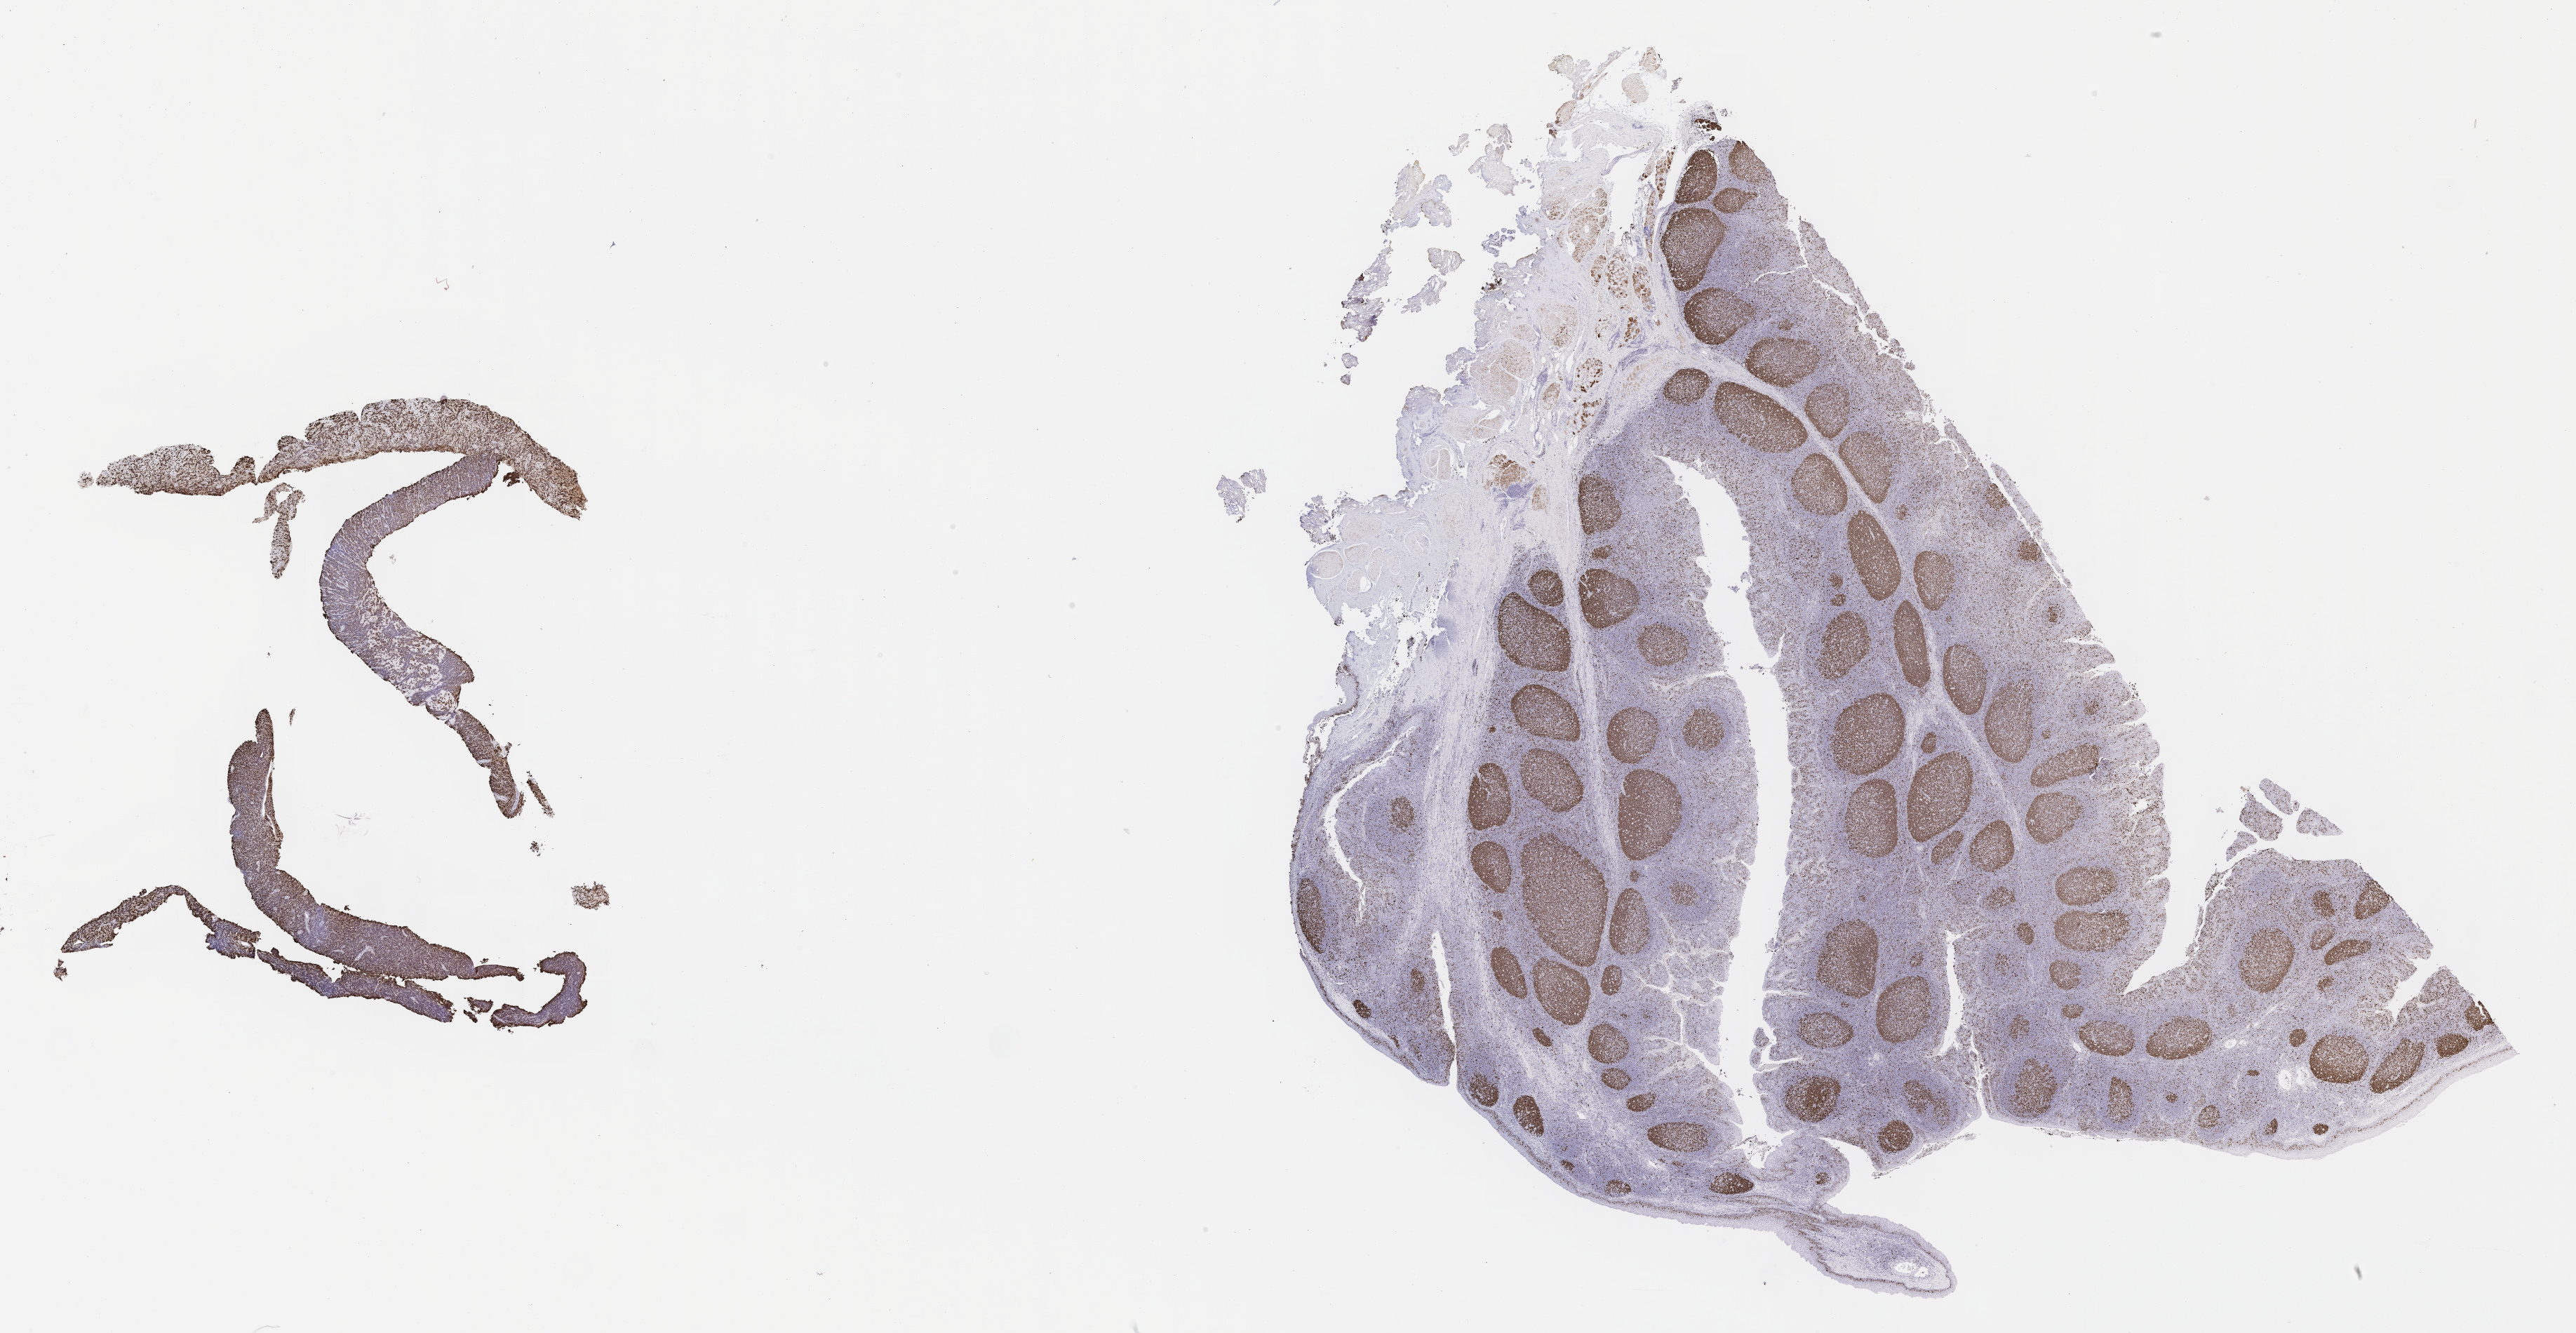
Whole-slide image, immunohistochemical stain for Ki-67, shown as a low-resolution overview of the whole scanned area (about 29.7 x 15.4 mm). Specimen: tumor tissue. Anatomic site: pleura. Male patient; age at initial diagnosis 2 years.
Histologic diagnosis: Diffuse large B-cell lymphoma, NOS.